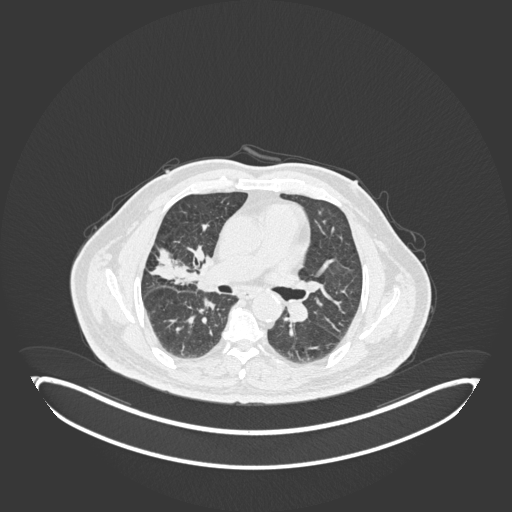
Chest CT, one axial slice; position 91 of 247 along the scan axis; reconstruction kernel B30f; 120 kVp; lung window (W 1500 / L -600 HU); 1 mm slice thickness; 512 × 512 image matrix, field of view 500 × 500 mm. Male patient, age 72 years. From the clinical record (not read from this slice): clinical TNM (as recorded): T1c N0 M0.
Outlined on this slice (bounding box drawn by a radiologist):
- lung tumour (recorded histology: squamous cell carcinoma): bounding box <183,239,216,296> (left, top, right, bottom; pixels)